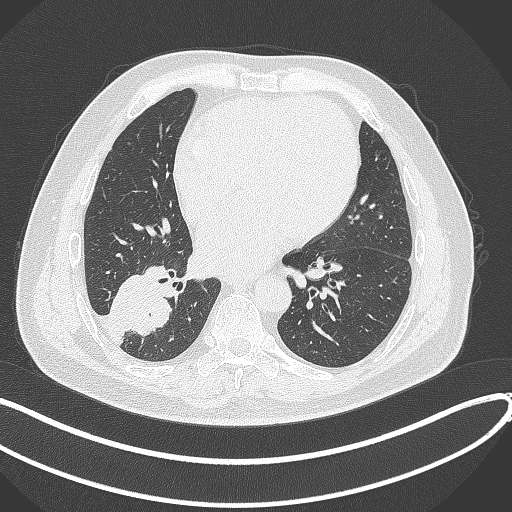
Chest CT, one axial slice. Position 147 of 360 along the scan axis. Lung window (W 1500 / L -600 HU). 1 mm slice thickness. 512 × 512 image matrix. Patient: male, 59 years.
Outlined on this slice (bounding box drawn by a radiologist):
- lung tumour (recorded histology: adenocarcinoma): bounding box (x1, y1, x2, y2) in pixels: (110, 257, 175, 337)